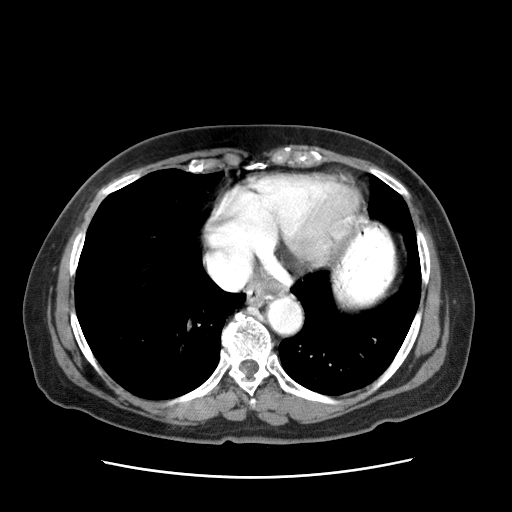
Contrast-enhanced abdominal CT (liver protocol), one axial slice; position 63 of 63 along the scan axis; reconstruction kernel STANDARD; 120 kVp; soft-tissue window (W 400 / L 40 HU); 2.5 mm slice thickness; 512 × 512 image matrix, field of view 360 × 360 mm. Patient: female, 79 years. Case-level facts recorded for this patient, not image findings: diagnosis: hepatocellular carcinoma (patient treated with transarterial chemoembolisation; whether this scan precedes or follows treatment is not stated here); TNM stage (as recorded): Stage-II; Child-Pugh class: B; tumour differentiation: well differentiated; tumour size: 5 cm.
Structures marked on this image (semi-automatic segmentation, software-assisted and operator-edited):
- abdominal aorta: bounding box (x1, y1, x2, y2) in pixels: (267, 297, 302, 335)